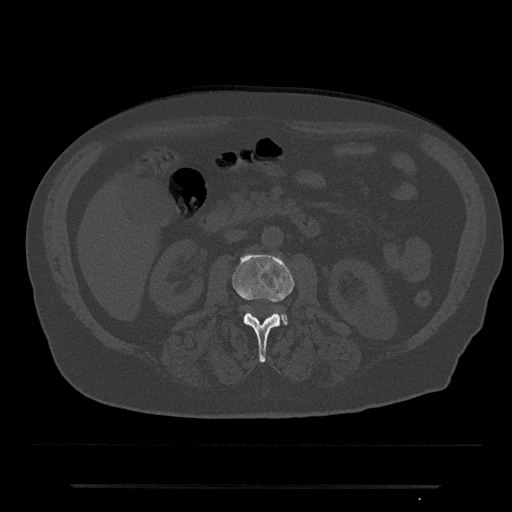
CT including the spine, one axial slice; slice 455 of 797 in the series (ordered by position); 120 kVp; bone window (W 1800 / L 400 HU); 0.5 mm slice thickness; 512 × 512 image matrix, field of view 434 × 434 mm. Patient: male, 80 years. From the clinical record (not read from this slice): primary cancer: prostate; vertebrae with lytic lesions (as recorded): L1, T11.
Structures marked on this image (semi-automatically segmented with operator editing):
- L2 vertebra: bounding box <232,254,294,363> (left, top, right, bottom; pixels)
- L3 vertebra: <277,311,288,325>